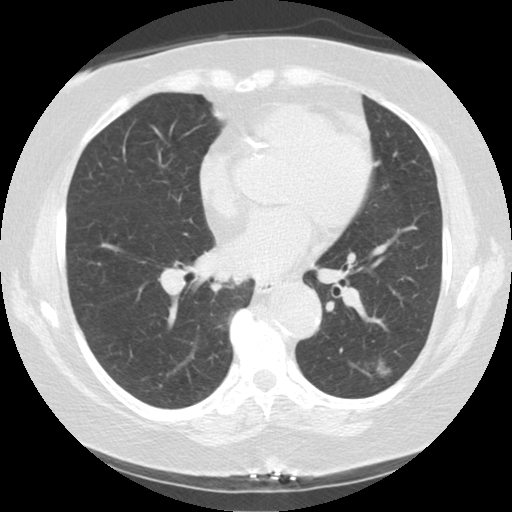
Low-dose screening chest CT, one axial slice. Position 63 of 122 along the scan axis. Lung window (W 1500 / L -600 HU). 2.5 mm slice thickness. 512 × 512 image matrix.
Annotated regions visible in this slice (expert manual segmentation):
- lesion 1 (tumor, lower lobe of left lung): bounding box (x1, y1, x2, y2) in pixels: (377, 361, 390, 376)